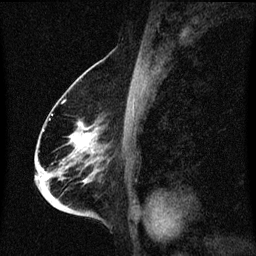
Breast MRI (dynamic contrast-enhanced), one sagittal slice. Position 38 of 60 along the scan axis. Dynamic contrast-enhanced series, image 2 of 3 at this slice position (ordered by acquisition). 1.5 T. TE 4.2 ms, TR 8.4 ms. 2 mm slice thickness. 256 × 256 image matrix, field of view 200 × 200 mm. Patient: female, 68 years. Case-level facts recorded for this patient, not image findings: setting: breast cancer imaged before/during neoadjuvant chemotherapy; receptor status: triple-negative.
Structures marked on this image (semi-automatically segmented with operator editing):
- analysis volume of interest (the breast-tissue region the enhancement analysis was run in; not a lesion): bounding box <37,96,113,213> (left, top, right, bottom; pixels)
- tumour enhancement mask (voxels above the 70 % enhancement threshold inside the analysis volume of interest): <71,124,93,183>